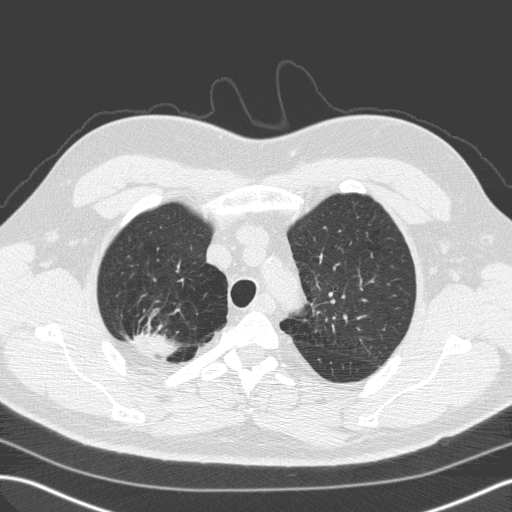
Low-dose screening chest CT, one axial slice. Slice 124 of 149 in the series (ordered by position). 120 kVp. Lung window (W 1500 / L -600 HU). 512 × 512 image matrix, field of view 357 × 357 mm.
Outlined on this slice (outlined manually by an expert reader):
- lesion 1 (tumor, upper lobe of right lung): box from (x=130, y=331) to (x=172, y=356) px